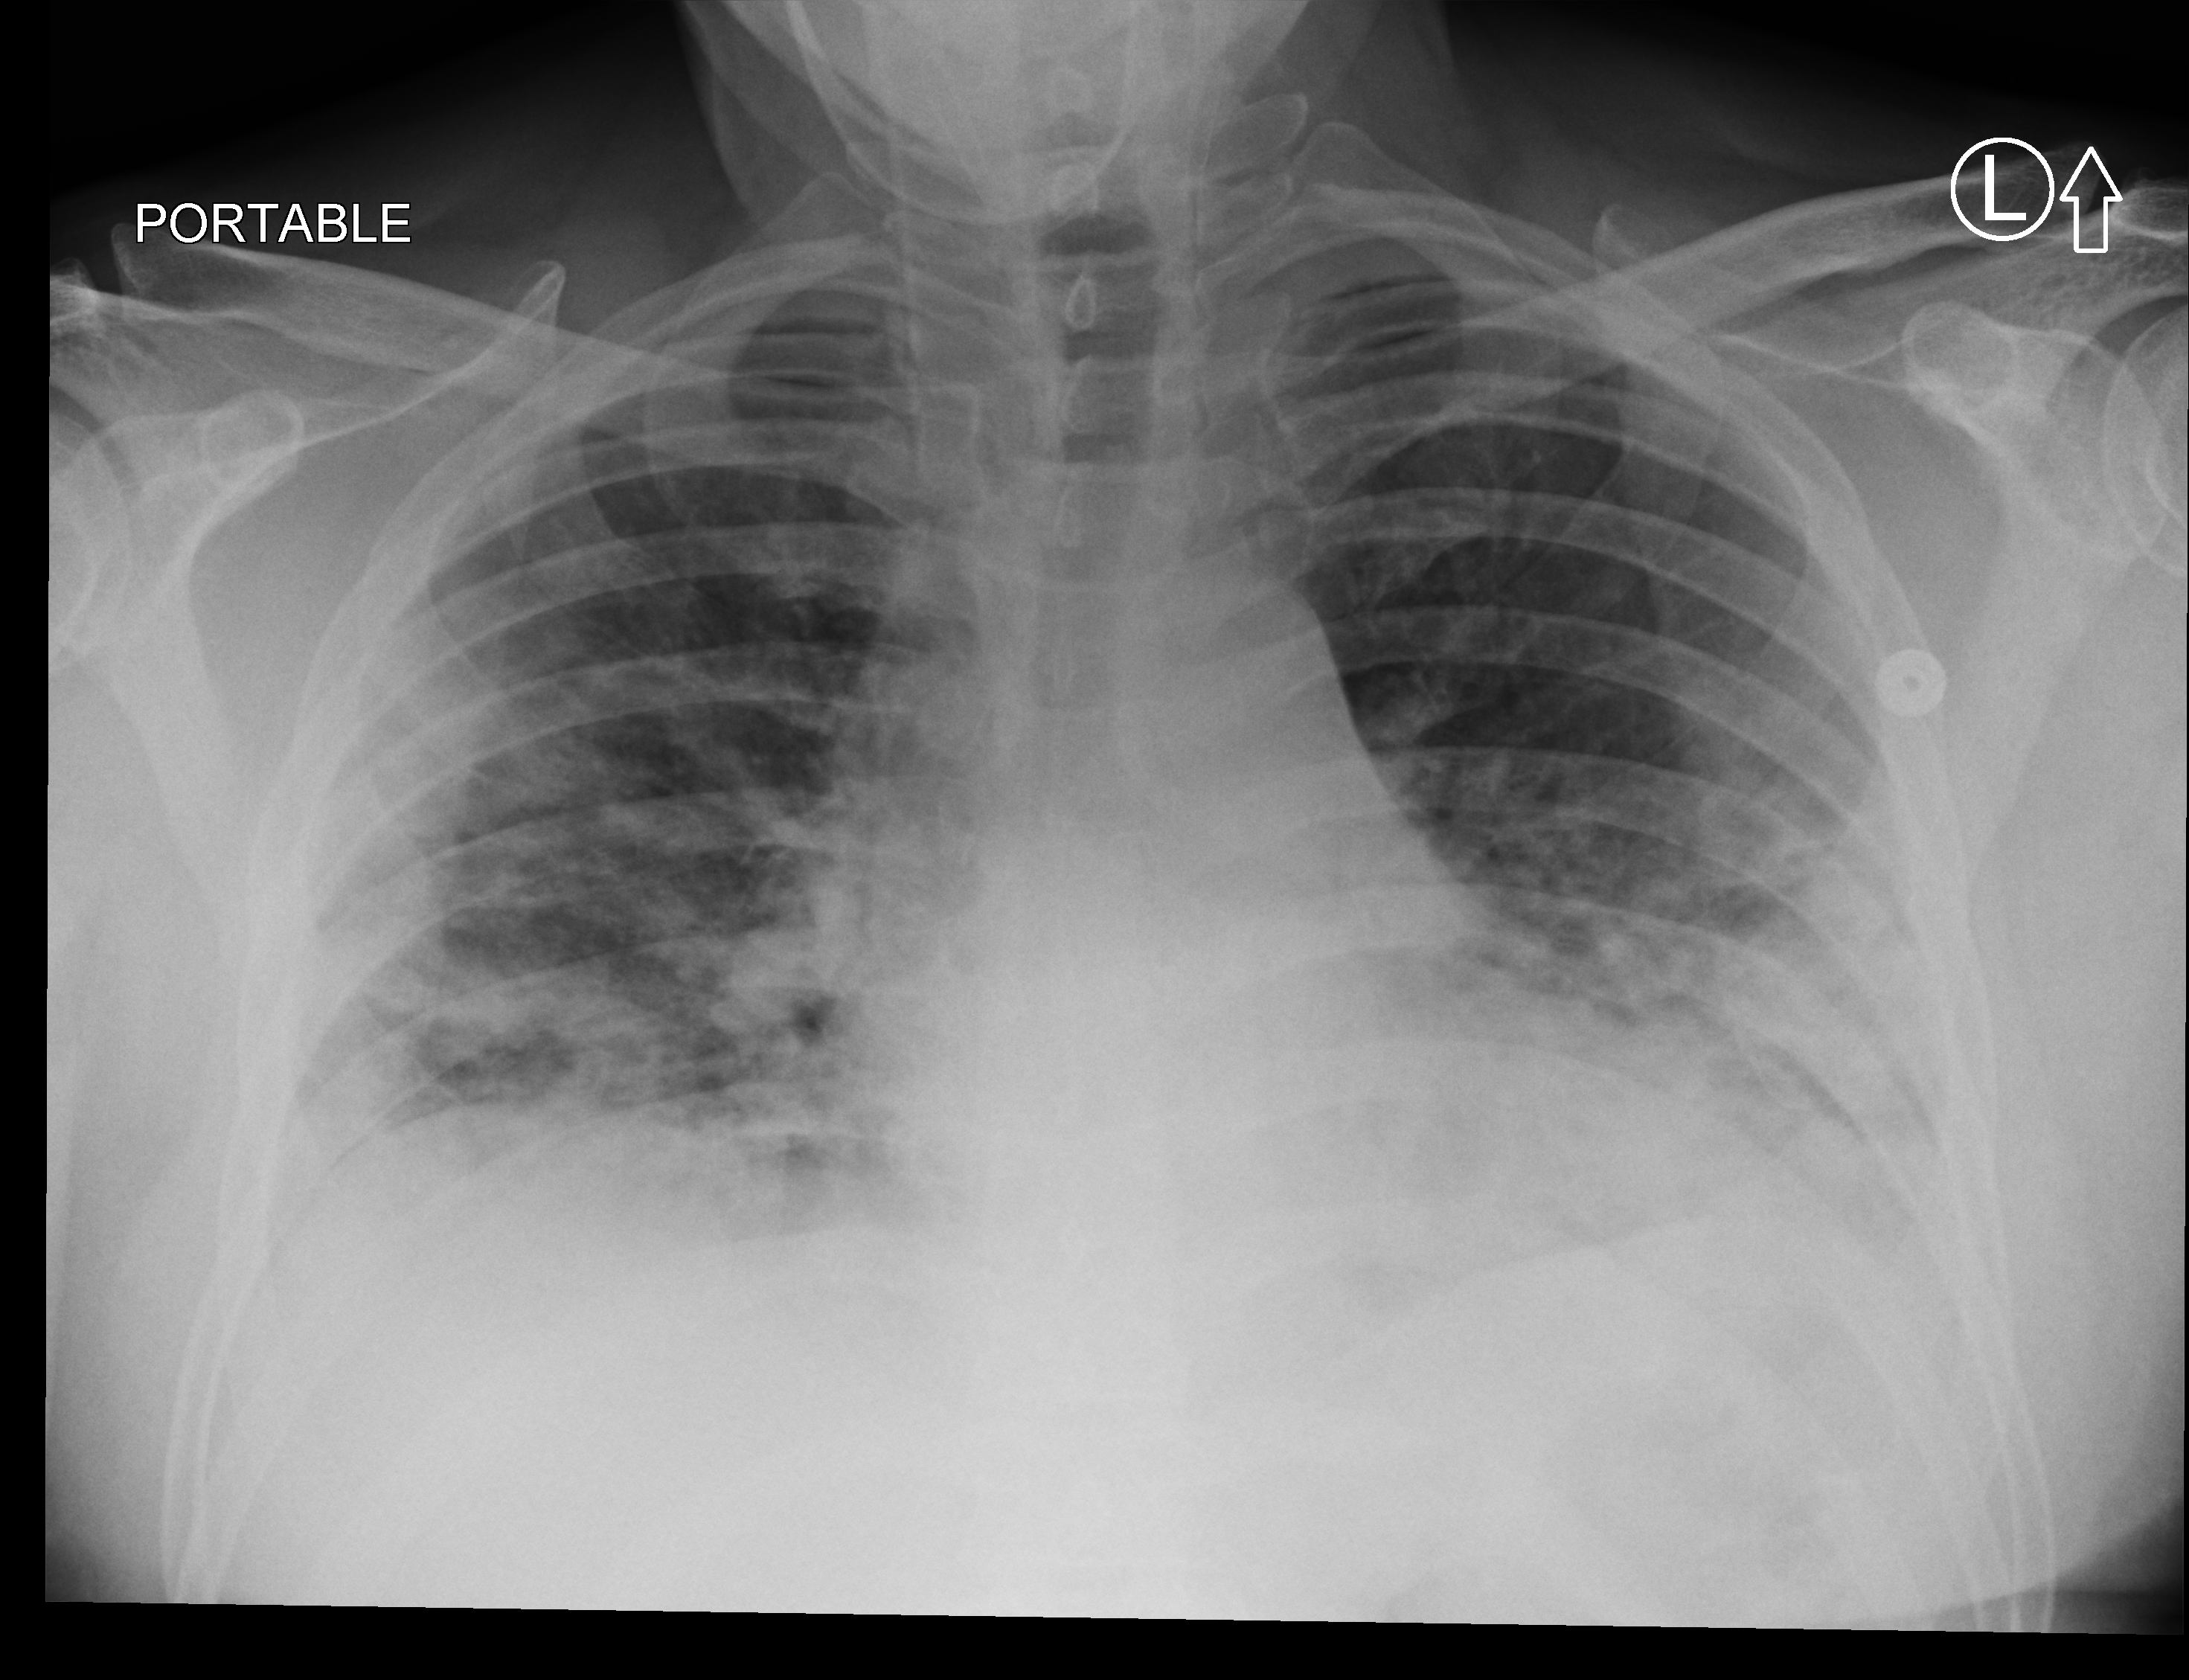
Bedside chest radiograph (computed radiography); anteroposterior (AP) projection. Male patient hospitalised with COVID-19, age 60–74 years.
Hospital-stay facts (about this admission, not read from this image; timing relative to this image not recorded): admitted to intensive care during this hospital stay: no; mechanically ventilated during this hospital stay: no.